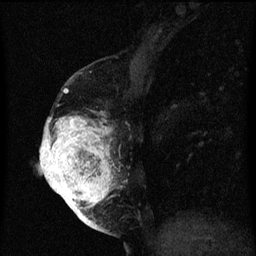
Breast MRI (dynamic contrast-enhanced), one sagittal slice; position 23 of 60 along the scan axis; dynamic contrast-enhanced series, image 2 of 3 at this slice position (ordered by acquisition); 1.5 T; TE 4.2 ms, TR 8 ms; 256 × 256 image matrix. Patient: female, 56 years.
Outlined on this slice (semi-automatic segmentation, software-assisted and operator-edited):
- analysis volume of interest (the breast-tissue region the enhancement analysis was run in; not a lesion): box from (x=40, y=112) to (x=121, y=219) px
- tumour enhancement mask (voxels above the 70 % enhancement threshold inside the analysis volume of interest): (x=40, y=118)–(x=115, y=219)